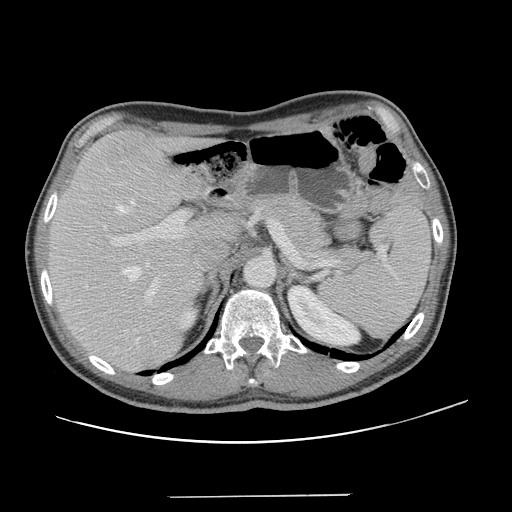
Contrast-enhanced abdominal CT, one axial slice. 120 kVp. Intravenous contrast given. Soft-tissue window (W 400 / L 40 HU). 512 × 512 image matrix, field of view 403 × 403 mm. Male patient, age 60 years. From the clinical record (not read from this slice): diagnosis: colorectal cancer liver metastases, imaged before liver resection; multiple liver metastases: no; largest metastasis: 2.5 cm; disease in both lobes: no.
Outlined on this slice (expert manual segmentation):
- hepatic veins: bounding box [x1, y1, x2, y2] px = [116, 199, 149, 281]
- liver: [48, 130, 233, 371]
- planned liver remnant (the part of the liver to remain after resection): [48, 130, 234, 355]
- portal vein (with intrahepatic branches): [101, 170, 195, 297]